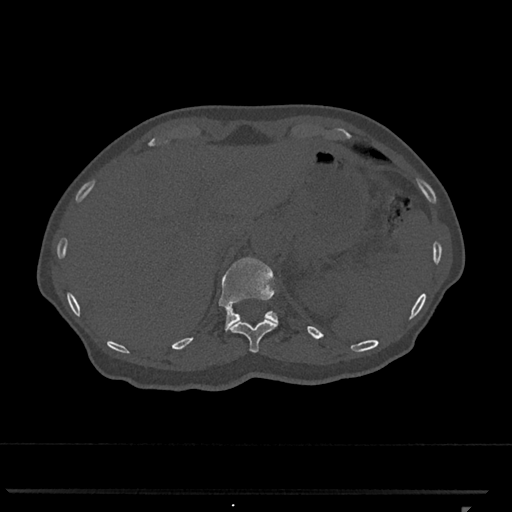
CT including the spine, one axial slice. Slice 493 of 793 in the series (ordered by position). Reconstruction kernel Br40s/3. Bone window (W 1800 / L 400 HU). 0.5 mm slice thickness. 512 × 512 image matrix, field of view 380 × 380 mm. Patient: female, 62 years. From the clinical record (not read from this slice): primary cancer: renal.
Structures marked on this image (semi-automatically segmented with operator editing):
- T11 vertebra: bounding box [x1, y1, x2, y2] px = [229, 319, 278, 353]
- T12 vertebra: [218, 257, 278, 333]